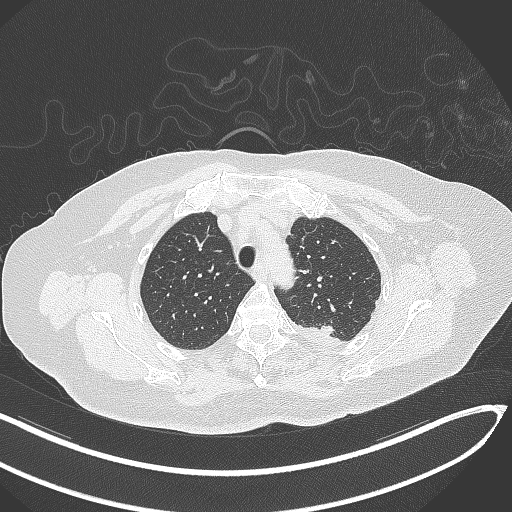
Chest CT, one axial slice; position 257 of 270 along the scan axis; reconstruction kernel B70f; lung window (W 1500 / L -600 HU); 1 mm slice thickness; 512 × 512 image matrix, field of view 400 × 400 mm. Patient: female, 76 years. Case-level facts recorded for this patient, not image findings: clinical TNM (as recorded): T1c N0 M0.
Structures marked on this image (bounding box drawn by a radiologist):
- lung tumour (recorded histology: adenocarcinoma): bounding box <312,318,337,341> (left, top, right, bottom; pixels)